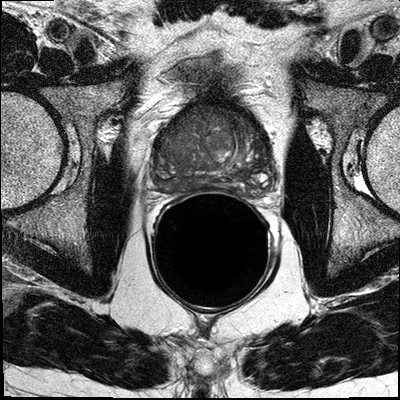
Prostate MRI examination; 3 images, each a single mid-volume slice chosen by position (not for content). Treatment context recorded for this patient: No surgery, patient was recommended casodex, leuprolide and radiation theraphy.
Image 1: T2-weighted axial slice, slice 17 of 32.
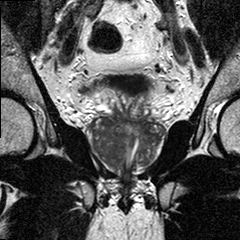
Image 2: T2-weighted coronal slice, series "T2W_TSE_COR", slice 13 of 24, 3 mm slice thickness.
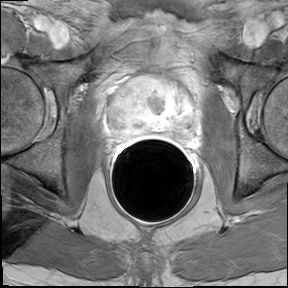
Image 3: DCE (dynamic gadolinium-enhanced) axial slice, series "AX BLISS_GAD_8", slice 17 of 32, dynamic phase 5 of 8, 6 mm slice thickness.
Report of this MRI examination:
FINDINGS: The prostate has a maximal lateral diameter of 5.5 cm, a maximal craniocaudal diameter of 3.7 cm and a maximal AP diameter of 3.9 cm resulting in an estimated gland volume of 41 cc. The zonal anatomy is preserved. Due to an enlarged right central gland the midline deviated to the left. There is a large right central gland tumor seen in the mid third and apical third of the prostate, involving on several levels nearly the entire right lobe. There is midline deviation with deviation and partial compression of the prostatic urethra. There is bulging towards the right inner obturator muscle. The tumor extends into the right posterior lateral and posterior peripheral zones bilateral. (at the midthird and apical level of the prostate). The tumor further extends anteriorly into the fibro-muscular band. At the right apex there is asymmetric suspiciously enhancing prostate tissue measuring 1.4 x 1.2 cm in transverse plane , highly suspicious for extraglandular extension. No evidence for manifest involvement of the neurovascular bundle on either side. No evidence for seminal vesicles infiltration. No evidence of involvement of bladder neck and rectal wall. No suspiciously enlarged obturator and iliac lymph nodes. No MRI evidence for involvement of osseous structures, as far as visualized. IMPRESSION: 1) Large predominantly right central gland tumor at midthird and apical third of prostate (as detailed above). Findings are suggestive for extracapsular extension at the right anterior lateral apex. (series 401, 601, 605, 606, slice location 21-27; annotations are saved on PACS). 2) No evidence for manifest involvement of the neurovascular bundle on either side. 3) No evidence for manifest seminal vesicles infiltration. 4) No evidence of involvement of bladder neck and rectal wall. 5) No suspiciously enlarged obturator and iliac lymph nodes. 6) No MRI evidence for malignant involvement of osseous structures, as far as visualized.

Biopsy pathology report for this patient (as recorded):
The specimen consists of multiple core fragments of tan soft tissue measuring 1.4cm to 2.1cm in length and 0.1cm in diameter. The specimen is submitted in six cassettes. 1-right pz, 2-right pz/tz, 3-right apex, 4-left pz, 5-left pz/tz, 6-left apex. PROSTATE 1. RIGHT PZ: PROSTATIC ADENOCARCINOMA, GLEASON SCORE 4+3=7/10, INVOLVING TWO OF TWO CORES, INVOLVING APPROXIMATELY 80% OF THE TISSUE SUBMITTED. 2. RIGHT PZ/TZ: PROSTATIC ADENOCARCINOMA, GLEASON SCORE 4+3=7/10, INVOLVING TWO OF TWO CORES, INVOLVING APPROXIMATELY 90% OF THE TISSUE SUBMITTED. 3. RIGHT APEX: PROSTATIC ADENOCARCINOMA, GLEASON SCORE 4+3=7/10, INVOLVING TWO OF TWO CORES, INVOLVING APPROXIMATELY 60% OF THE TISSUE SUBMITTED. 4. LEFT PZ: PROSTATIC ADENOCARCINOMA, GLEASON SCORE 3+4=7/10, INVOLVING TWO OF TWO CORES, INVOLVING APPROXIMATELY 20% OF THE TISSUE SUBMITTED. 5. LEFT PZ/TZ: PROSTATIC ADENOCARCINOMA, GLEASON SCORE 3+4=7/10, INVOLVING TWO OF TWO CORES, INVOLVING 20% OF THE TISSUE SUBMITTED. 6. LEFT APEX: PROSTATIC ADENOCARCINOMA, GLEASON SCORE 3+4=7/10, INVOLVING TWO OF TWO CORES, INVOLVING APPROXIMATELY 15% OF THE TISSUE SUBMITTED.